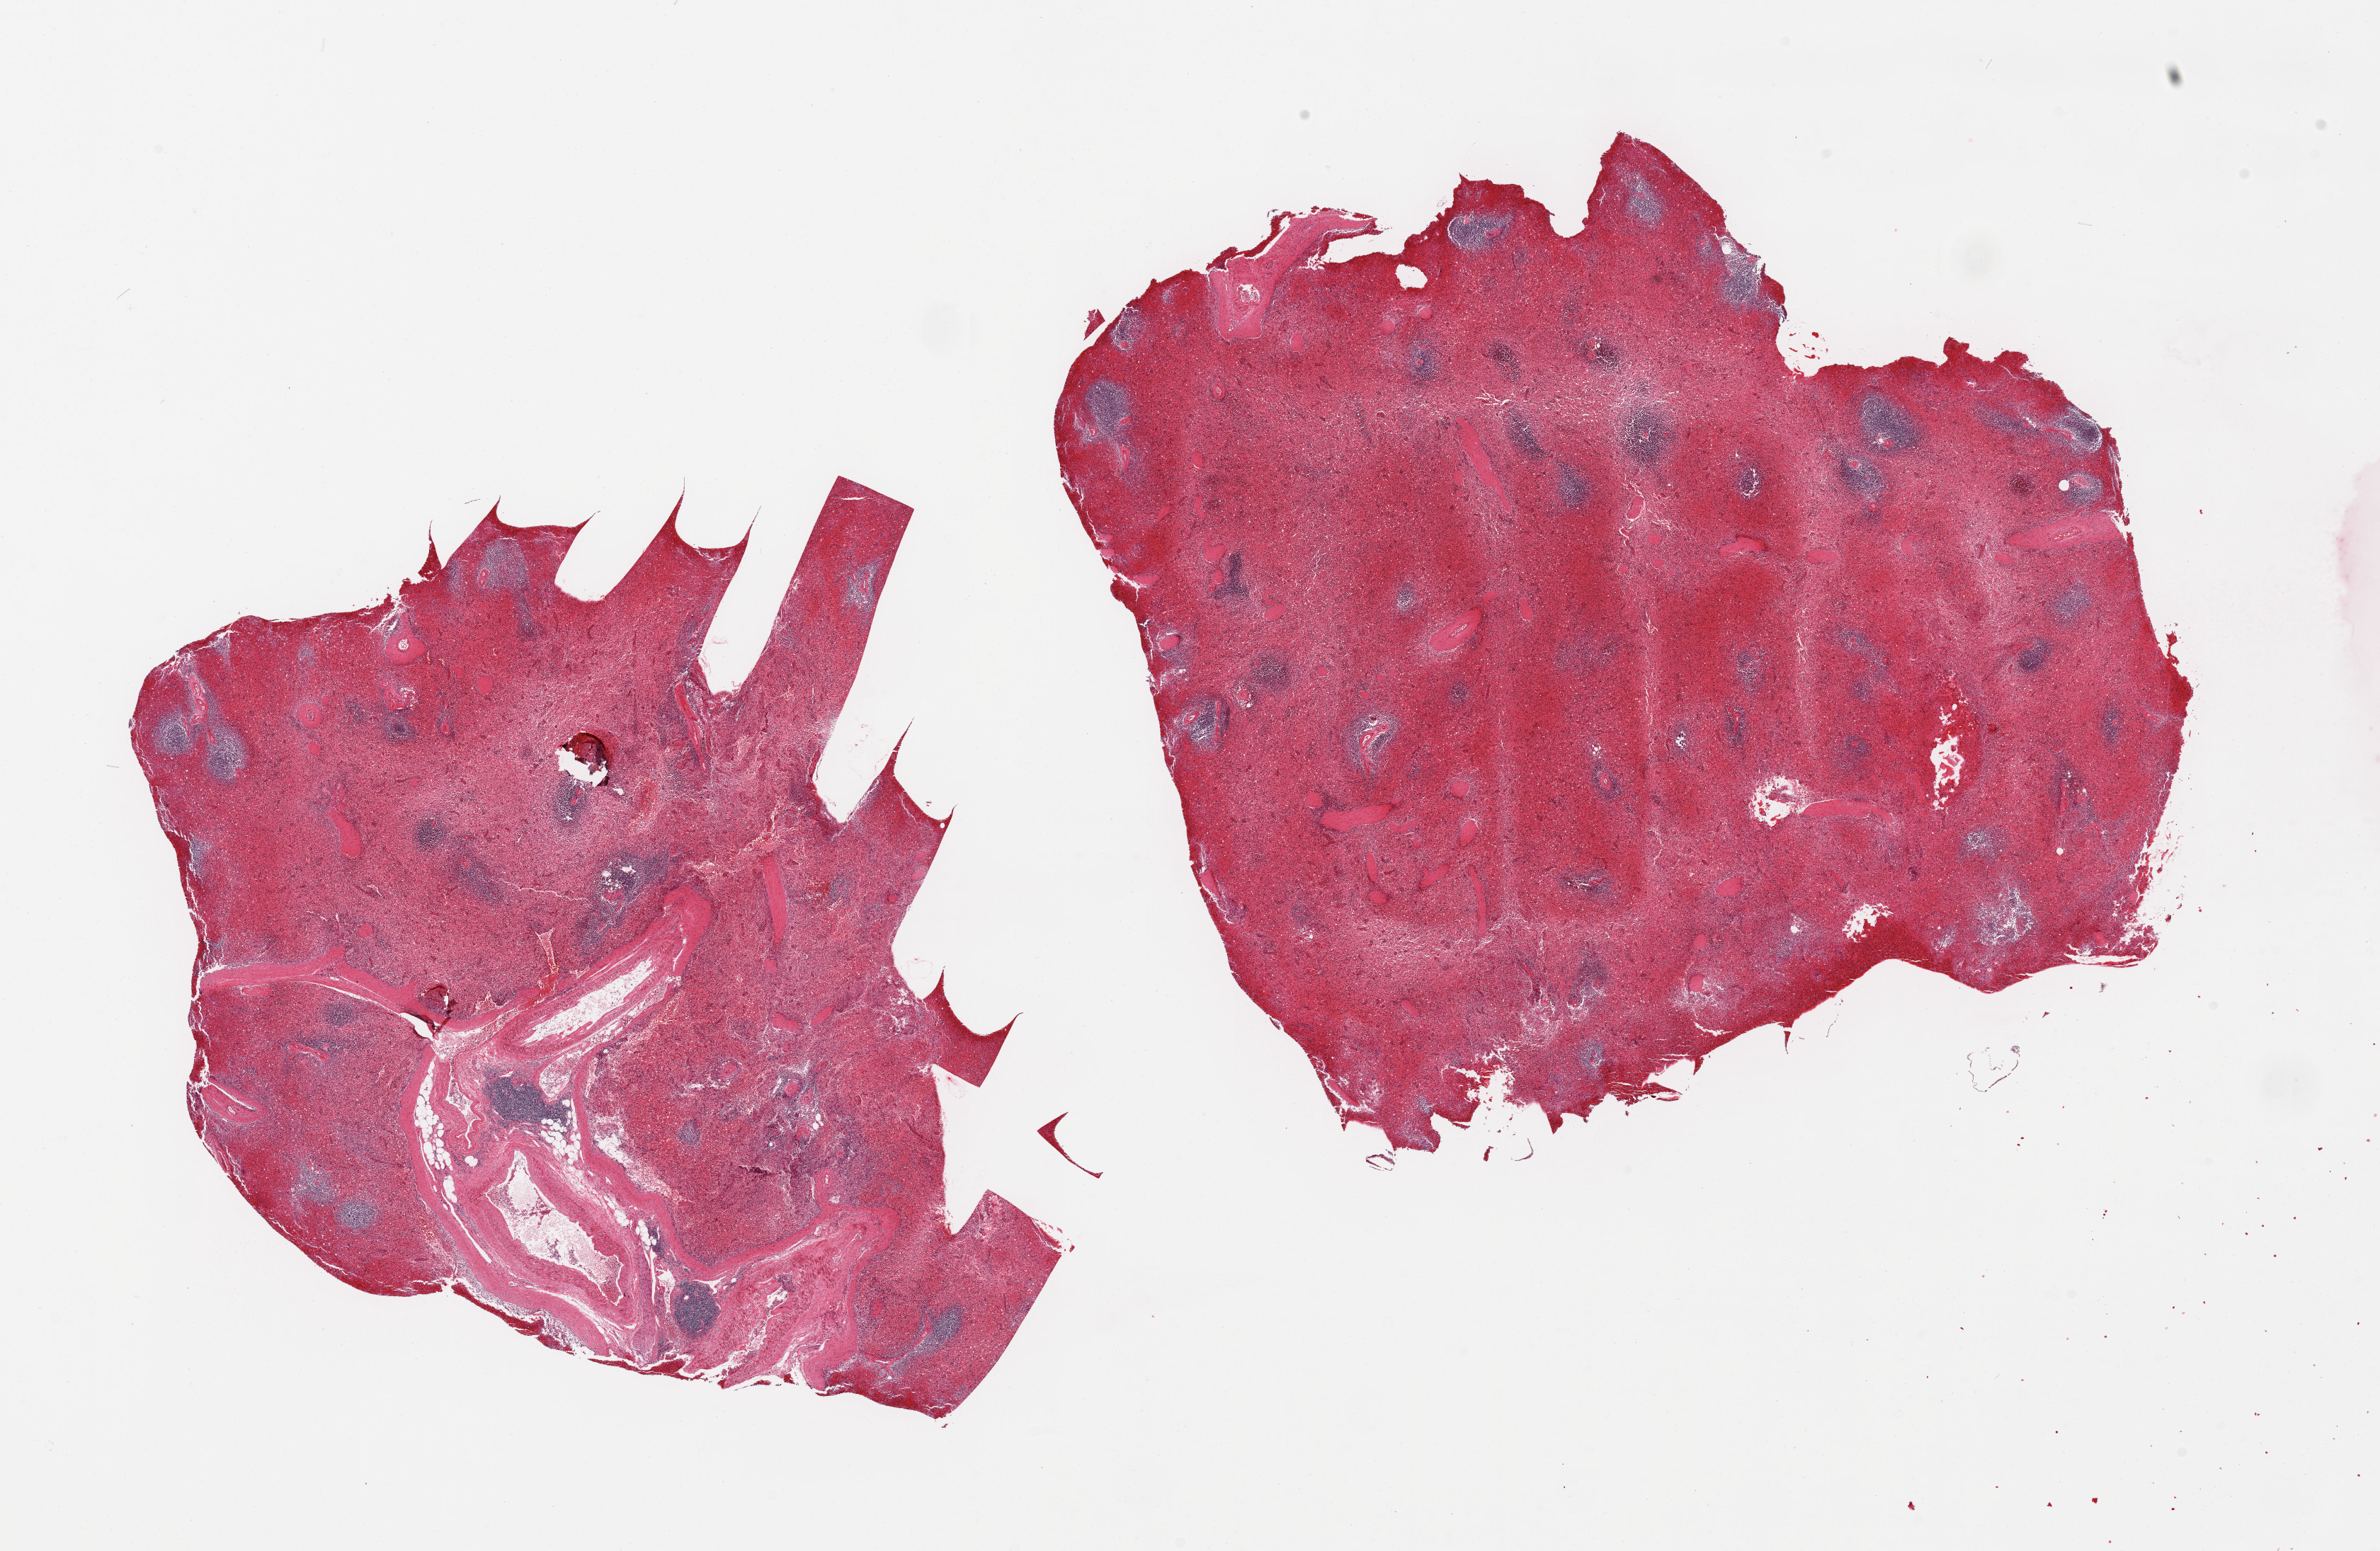
Digitized hematoxylin and eosin (H&E)-stained section, low-resolution overview of the scanned area, about 26.6 x 17.3 mm (slide scanned at 20x); PAXgene-fixed, paraffin-embedded tissue; section of spleen (target tissue); donor tissue sample. Donor sex: male.
Reviewer comment on this tissue sample: 2 pieces; 1 has 20% large blood vessels.